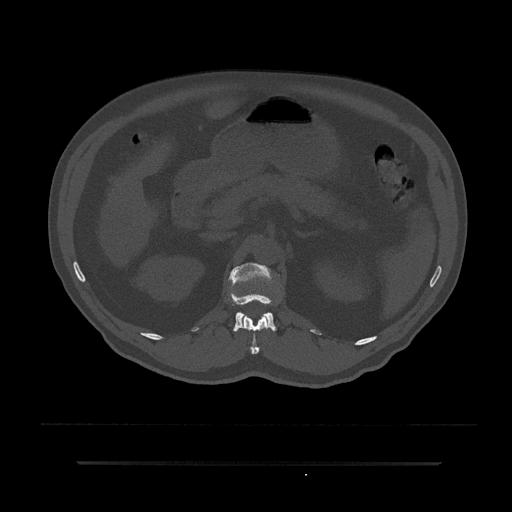
CT including the spine, one axial slice. Position 177 of 797 along the scan axis. Bone window (W 1800 / L 400 HU). 512 × 512 image matrix, field of view 464 × 464 mm. Male patient, age 59 years. From the clinical record (not read from this slice): primary cancer: bile ducts; vertebrae with lytic lesions (as recorded): T10.
Structures marked on this image (semi-automatically segmented with operator editing):
- L1 vertebra: bounding box <229,263,276,332> (left, top, right, bottom; pixels)
- T12 vertebra: <240,315,269,355>